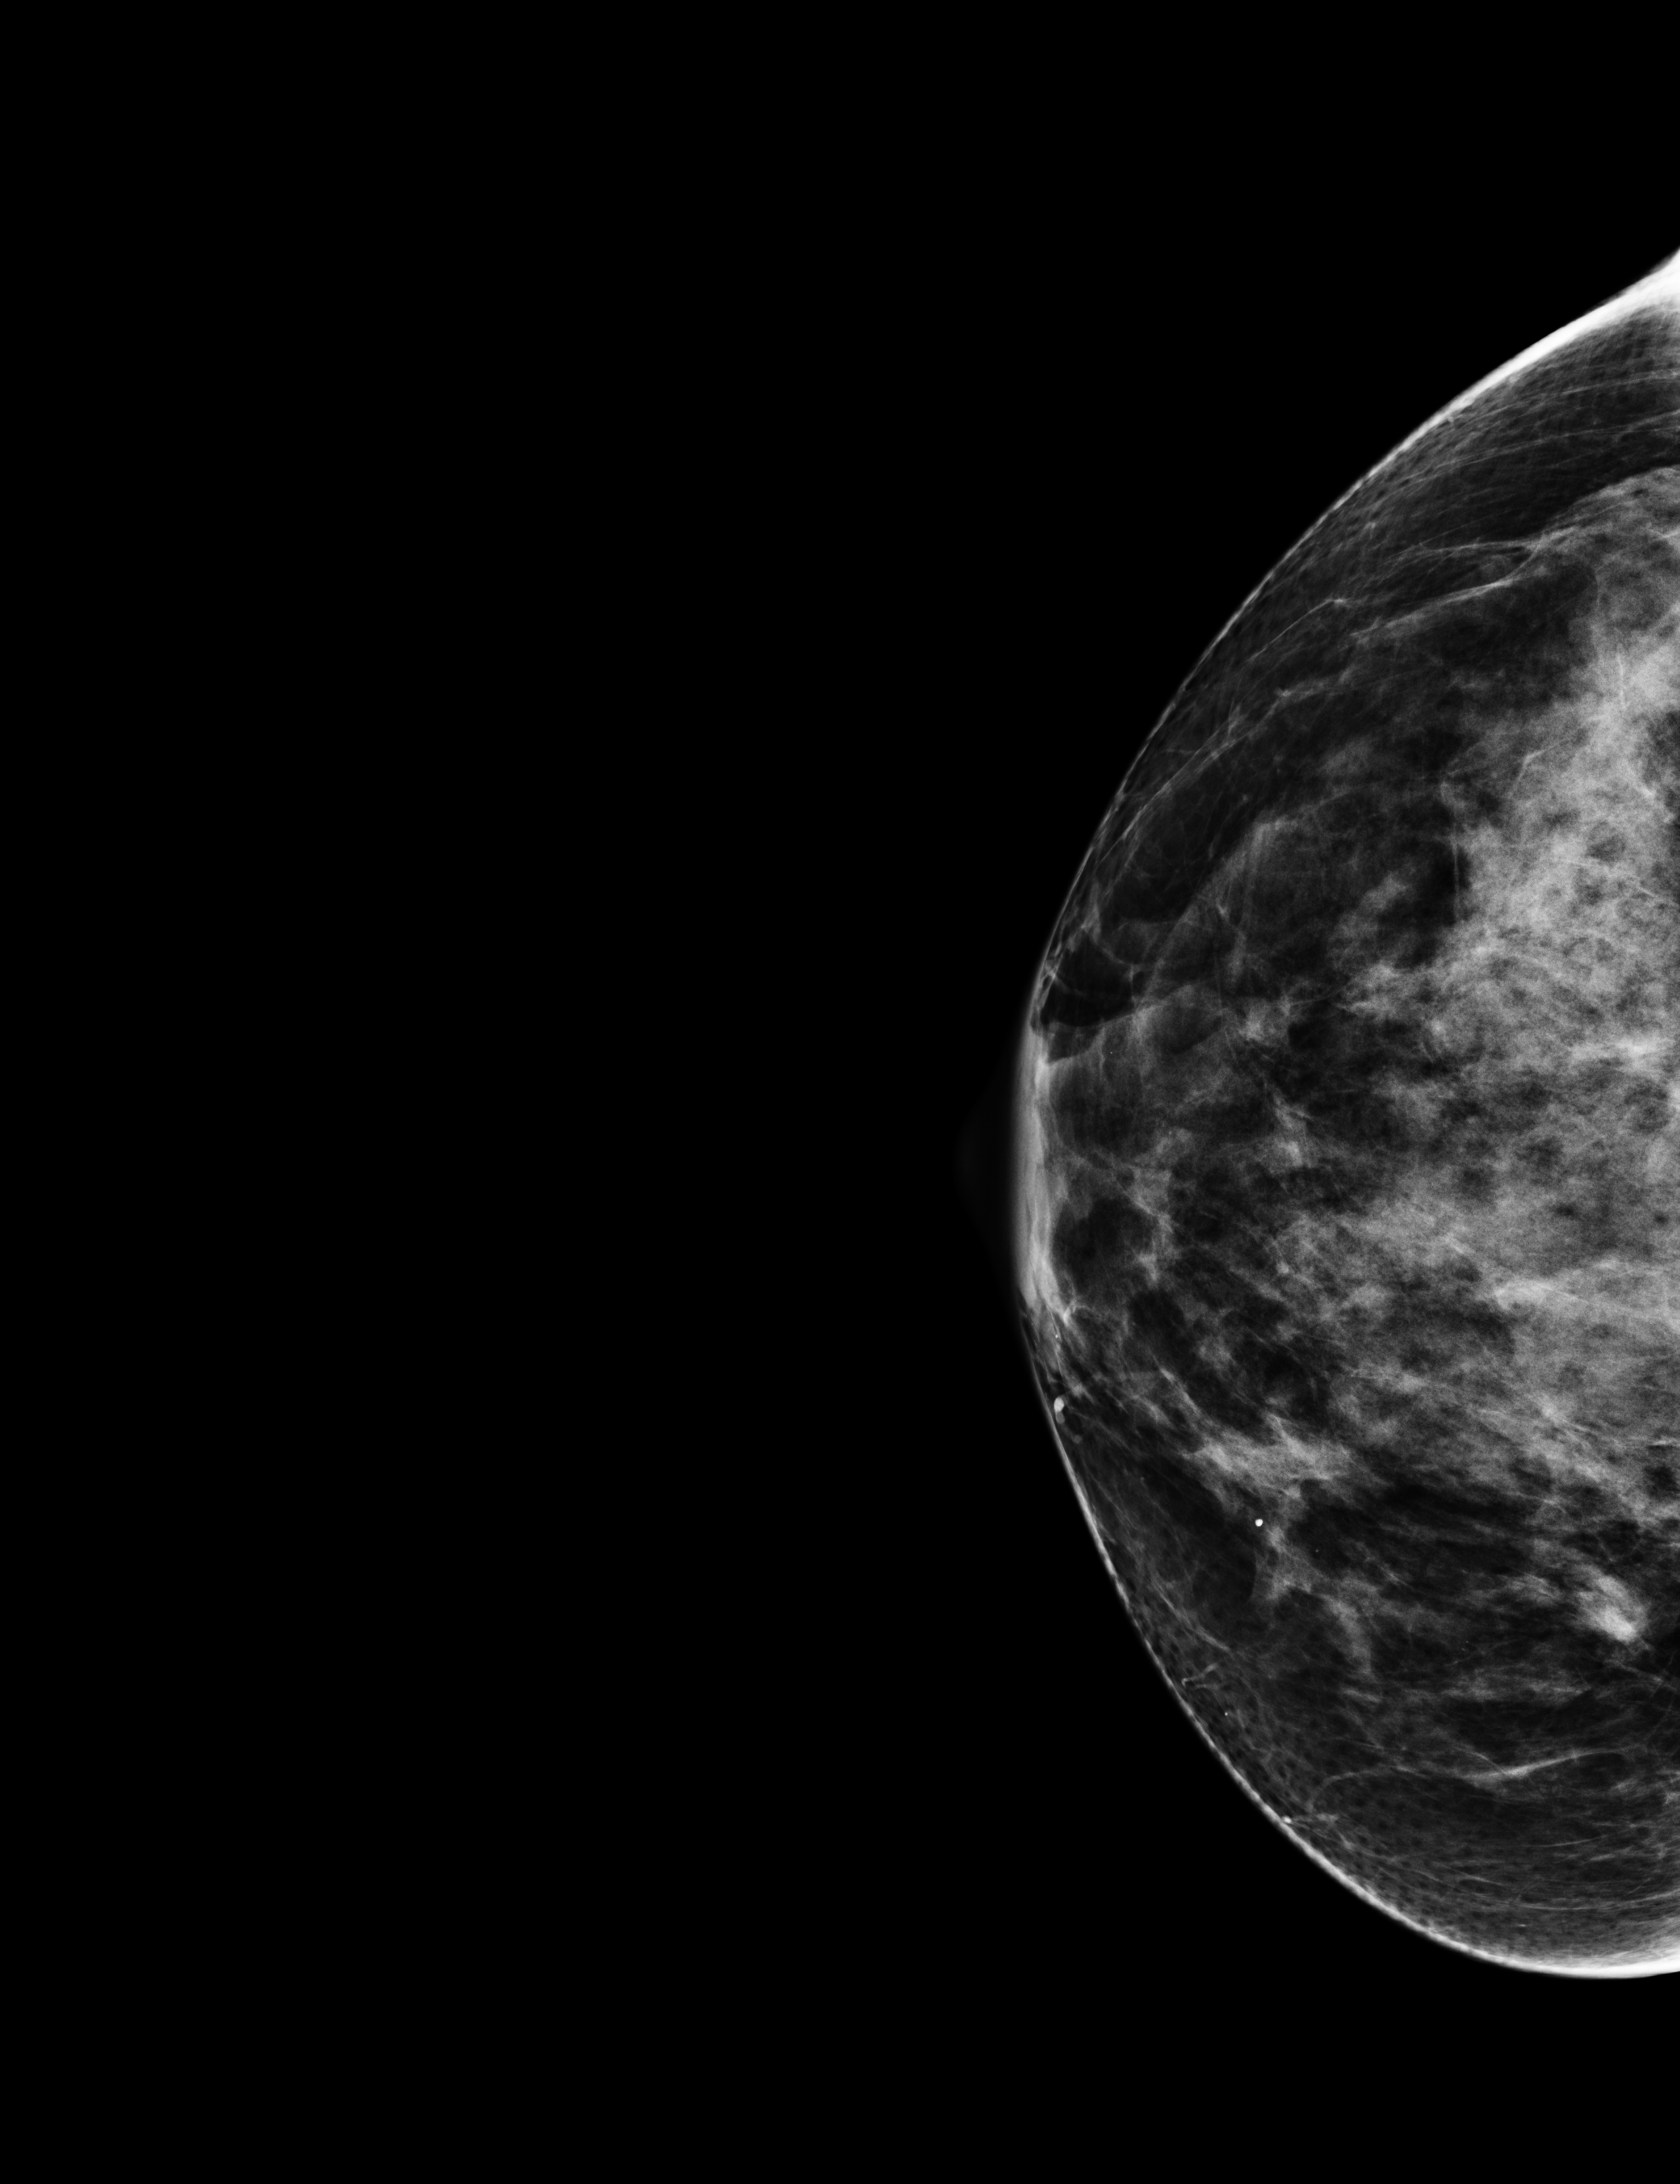
Digital mammogram (FFDM); right breast; cranio-caudal projection; annual screening mammography examination. Patient aged 64 years (female).
Final BI-RADS category for the screening round (tomosynthesis exam, both breasts): category 1.